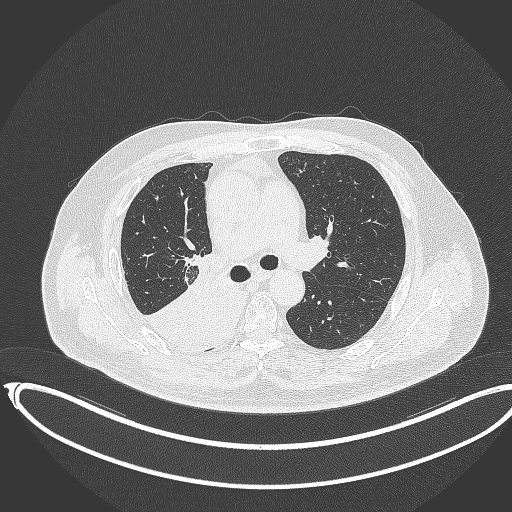
Chest CT, one axial slice; slice 223 of 403 in the series (ordered by position); lung window (W 1500 / L -600 HU); 1 mm slice thickness; 512 × 512 image matrix, field of view 436 × 436 mm. Male patient, age 68 years. Case-level facts recorded for this patient, not image findings: clinical TNM (as recorded): T2a N0 M0.
Structures marked on this image (bounding box drawn by a radiologist):
- lung tumour (recorded histology: adenocarcinoma): box from (x=144, y=259) to (x=241, y=350) px